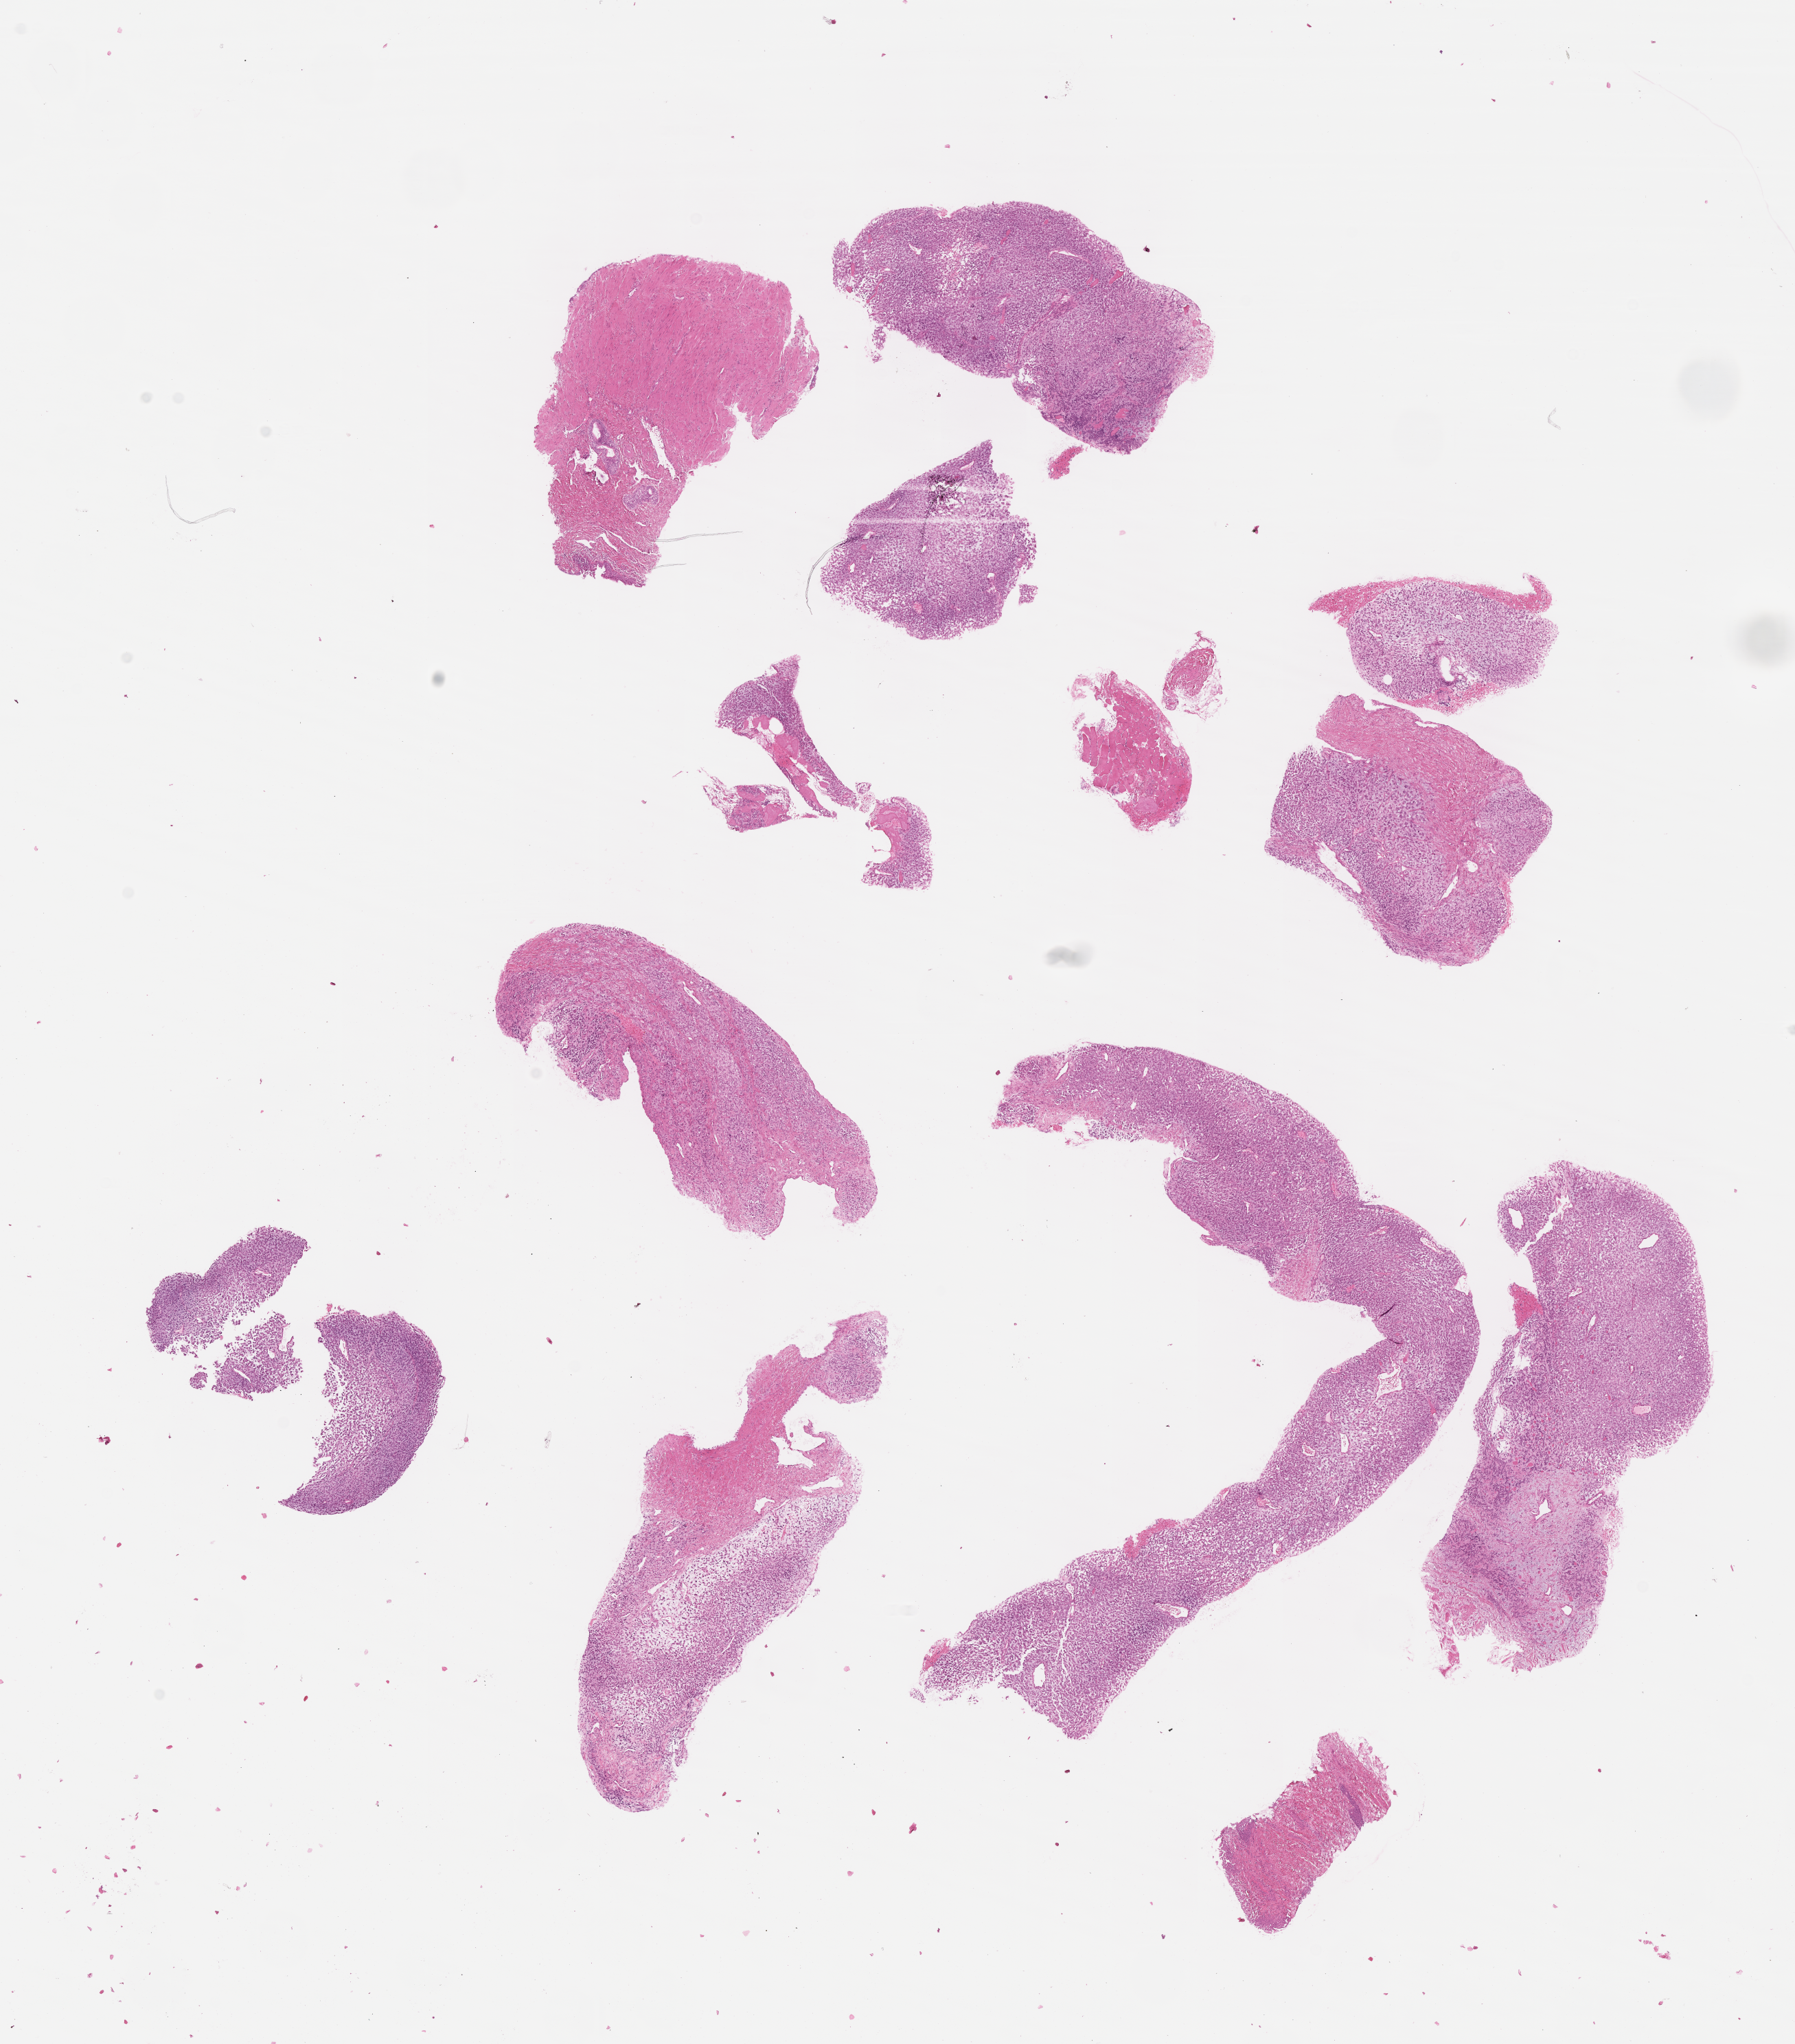
Digitized hematoxylin and eosin (H&E)-stained section of tumor tissue, whole scanned area (about 10.6 x 12.0 mm) shown as a low-resolution overview, formalin-fixed paraffin-embedded section, sample anatomic site: prostate. Male patient, age at diagnosis 11.7 years.
- metastatic status at presentation (as recorded): non-metastatic (unconfirmed)
- diagnosis: rhabdomyosarcoma; histological classification: embryonal rhabdomyosarcoma